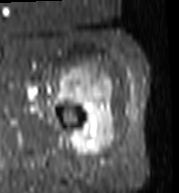
MRI of an extremity soft-tissue mass, one axial slice; position 87 of 103 along the scan axis; STIR; MR volume resampled by the dataset authors to the PET/CT grid (not the native acquisition matrix); 179 × 193 image matrix, field of view 175 × 188 mm. Female patient. Case-level facts recorded for this patient, not image findings: histological type: undifferentiated – high grade; grade: high; site of the primary tumour: left thigh.
Outlined on this slice (expert contour drawn on MRI and transferred to this co-registered scan by the dataset authors):
- gross tumour volume including surrounding oedema: bounding box <57,64,117,161> (left, top, right, bottom; pixels)
- gross tumour volume (mass): <59,66,115,157>